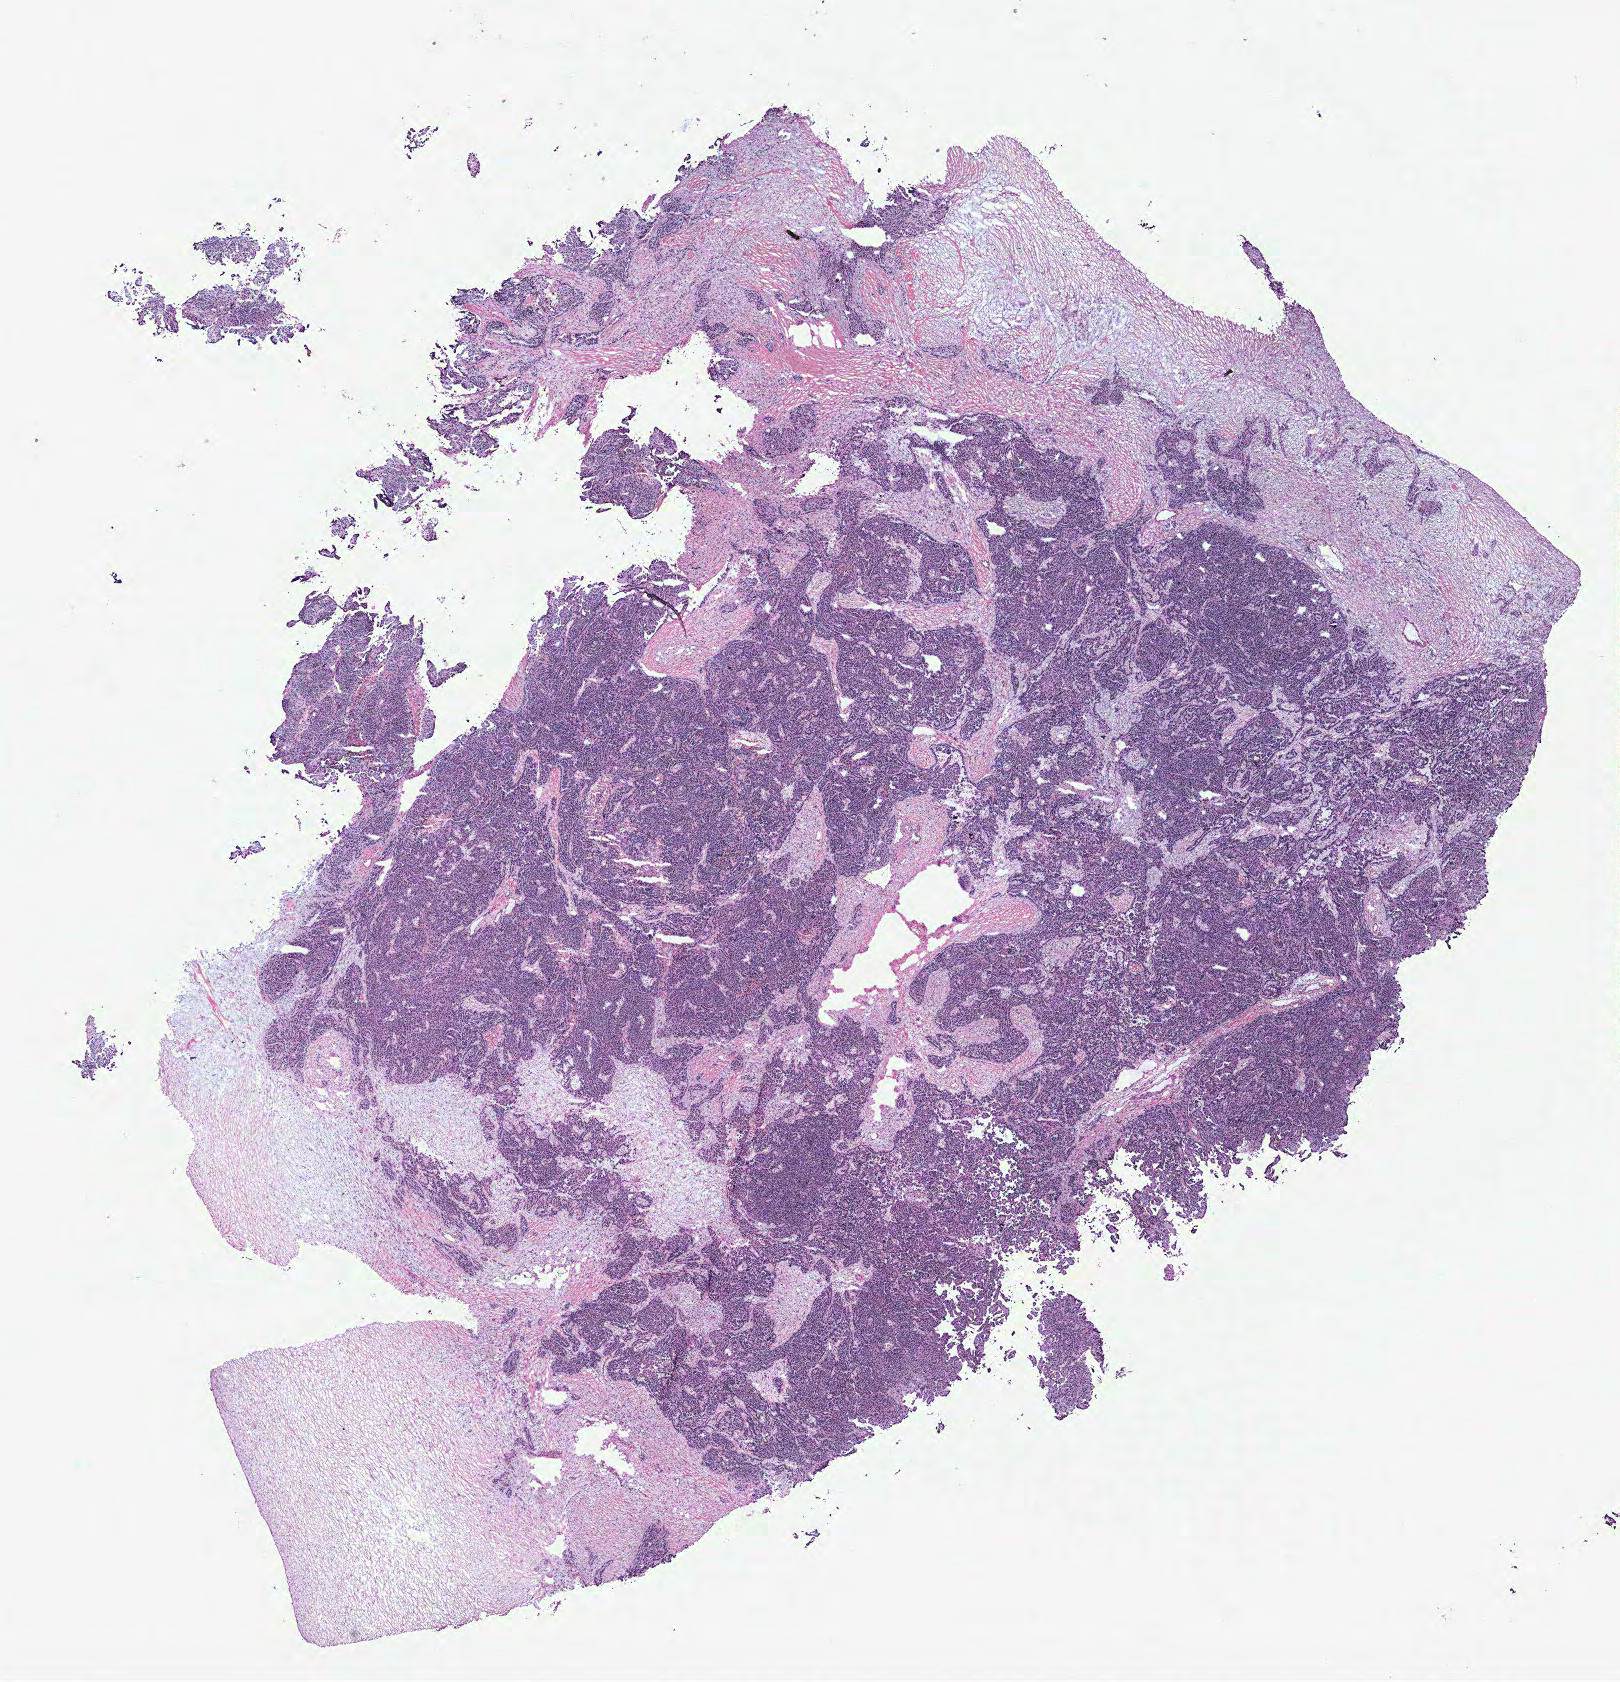
H&E-stained whole-slide image, shown as a low-resolution overview of the whole scanned area (about 13.0 x 13.5 mm, slide scanned at 40x); ovary, tumour tissue. Patient: female, age 65 years.
Primary tumour site (as recorded): ovary. Histologic diagnosis: Serous adenocarcinoma, NOS.